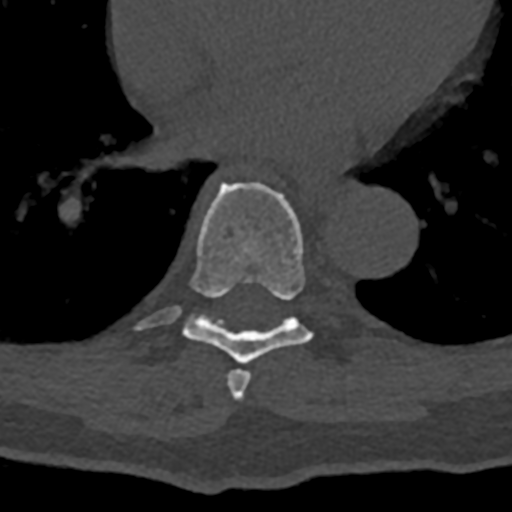
CT including the spine, one axial slice. Slice 706 of 797 in the series (ordered by position). Reconstruction kernel Br40s/3. 120 kVp. Bone window (W 1800 / L 400 HU). 0.5 mm slice thickness. 512 × 512 image matrix, field of view 160 × 160 mm. Patient: male, 74 years. From the clinical record (not read from this slice): primary cancer: renal; vertebrae with lytic lesions (as recorded): T10, L1, L2, L3, L4, L5.
Structures marked on this image (semi-automatic segmentation, software-assisted and operator-edited):
- T7 vertebra: bounding box <227,370,251,401> (left, top, right, bottom; pixels)
- T8 vertebra: <134,182,323,364>